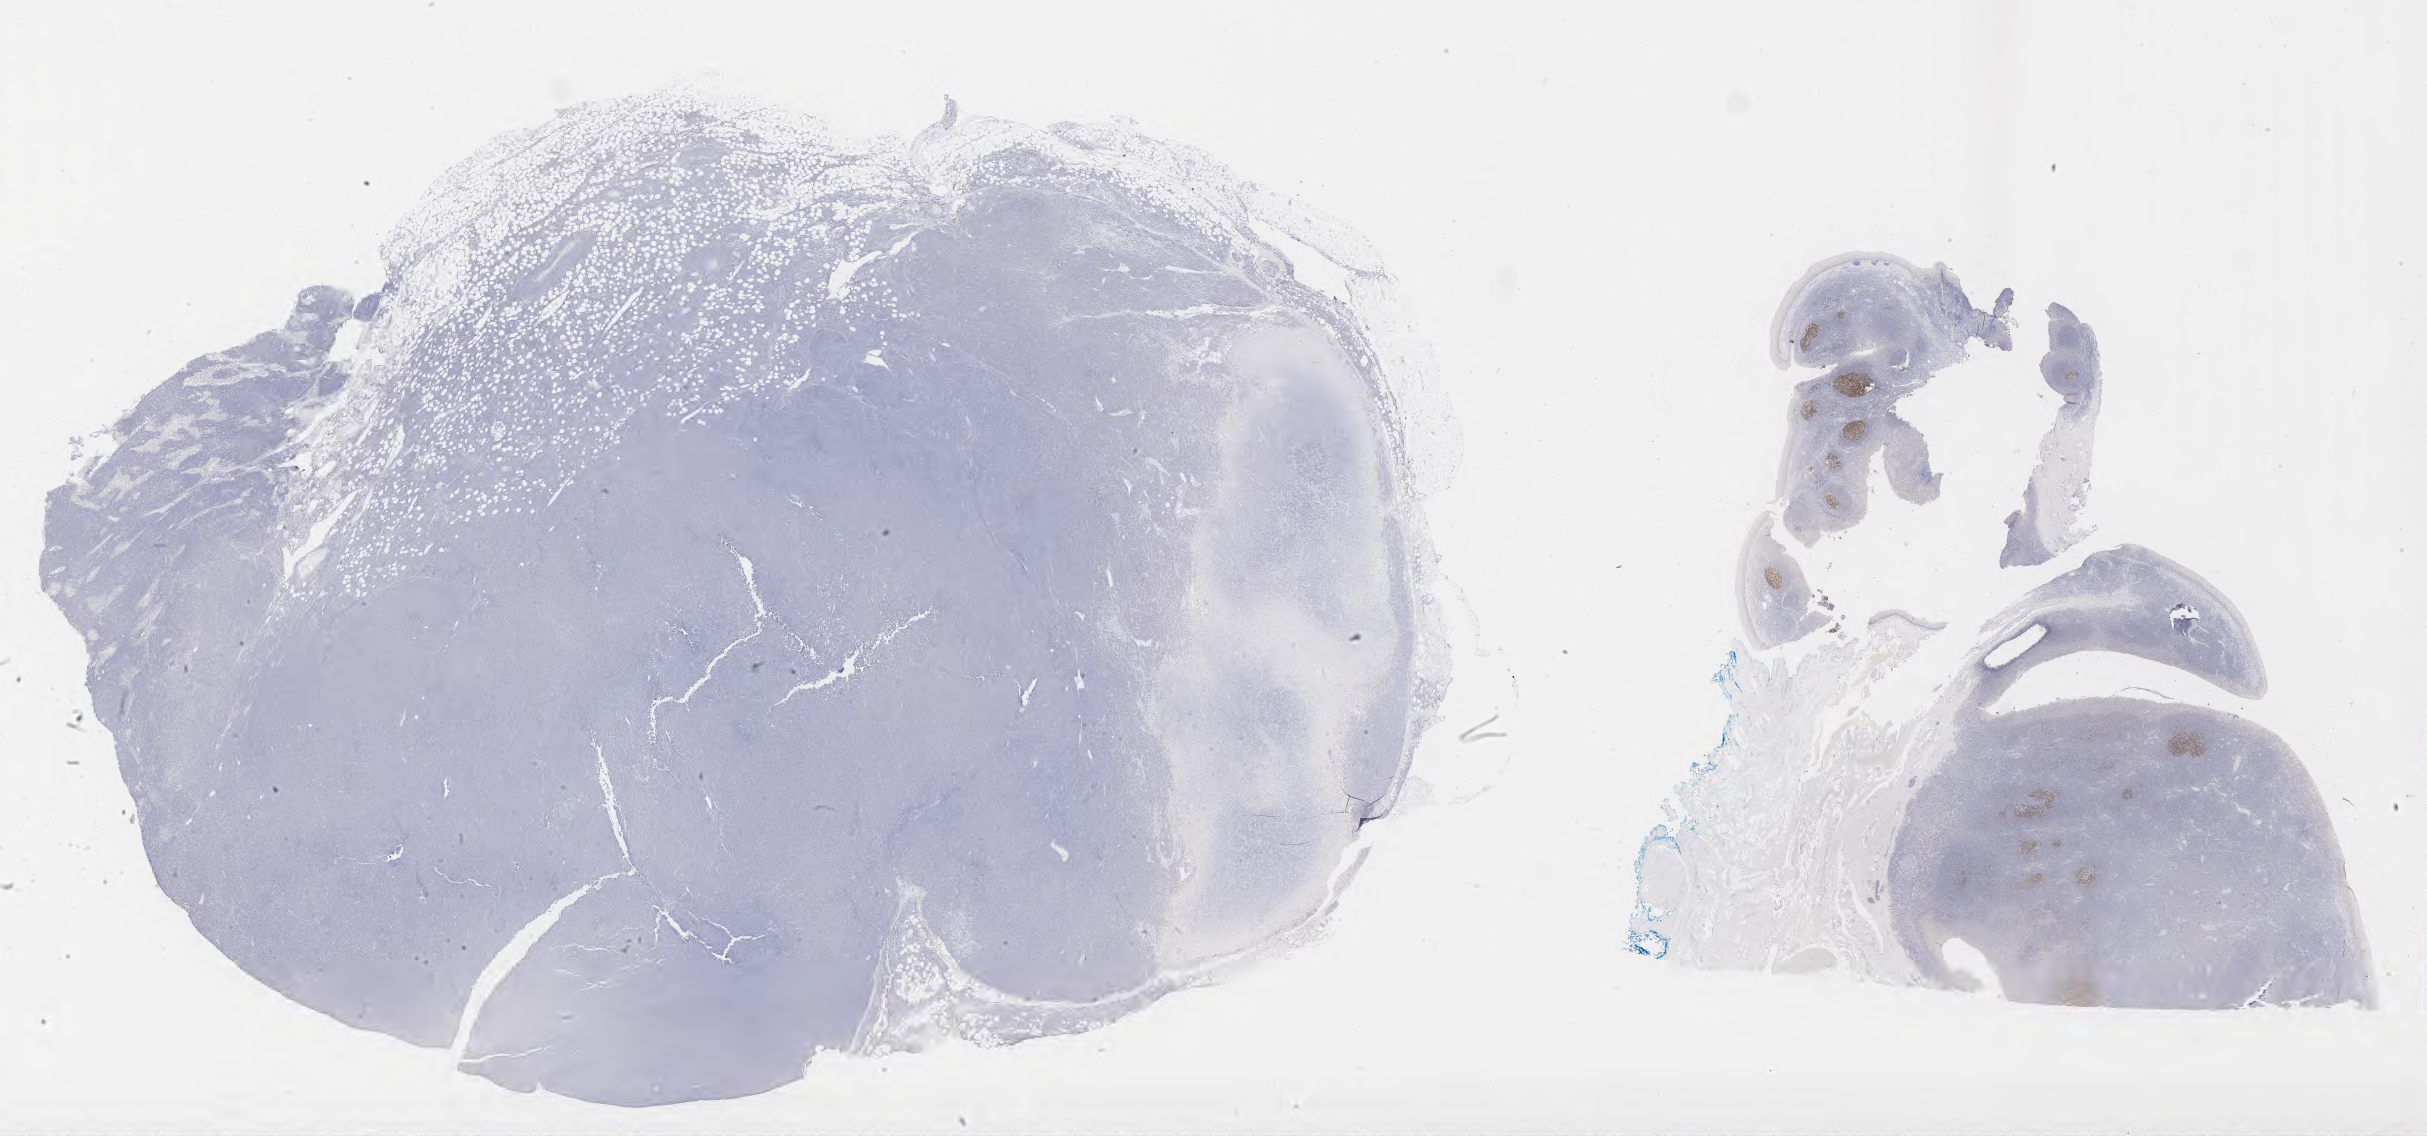
Immunohistochemistry (IHC) whole-slide image stained for BCL6, shown as a low-resolution overview of the whole scanned area (about 39.2 x 18.4 mm). Specimen: tumor tissue. Patient: male, 57 years old.
Histologic diagnosis: Burkitt lymphoma, NOS.